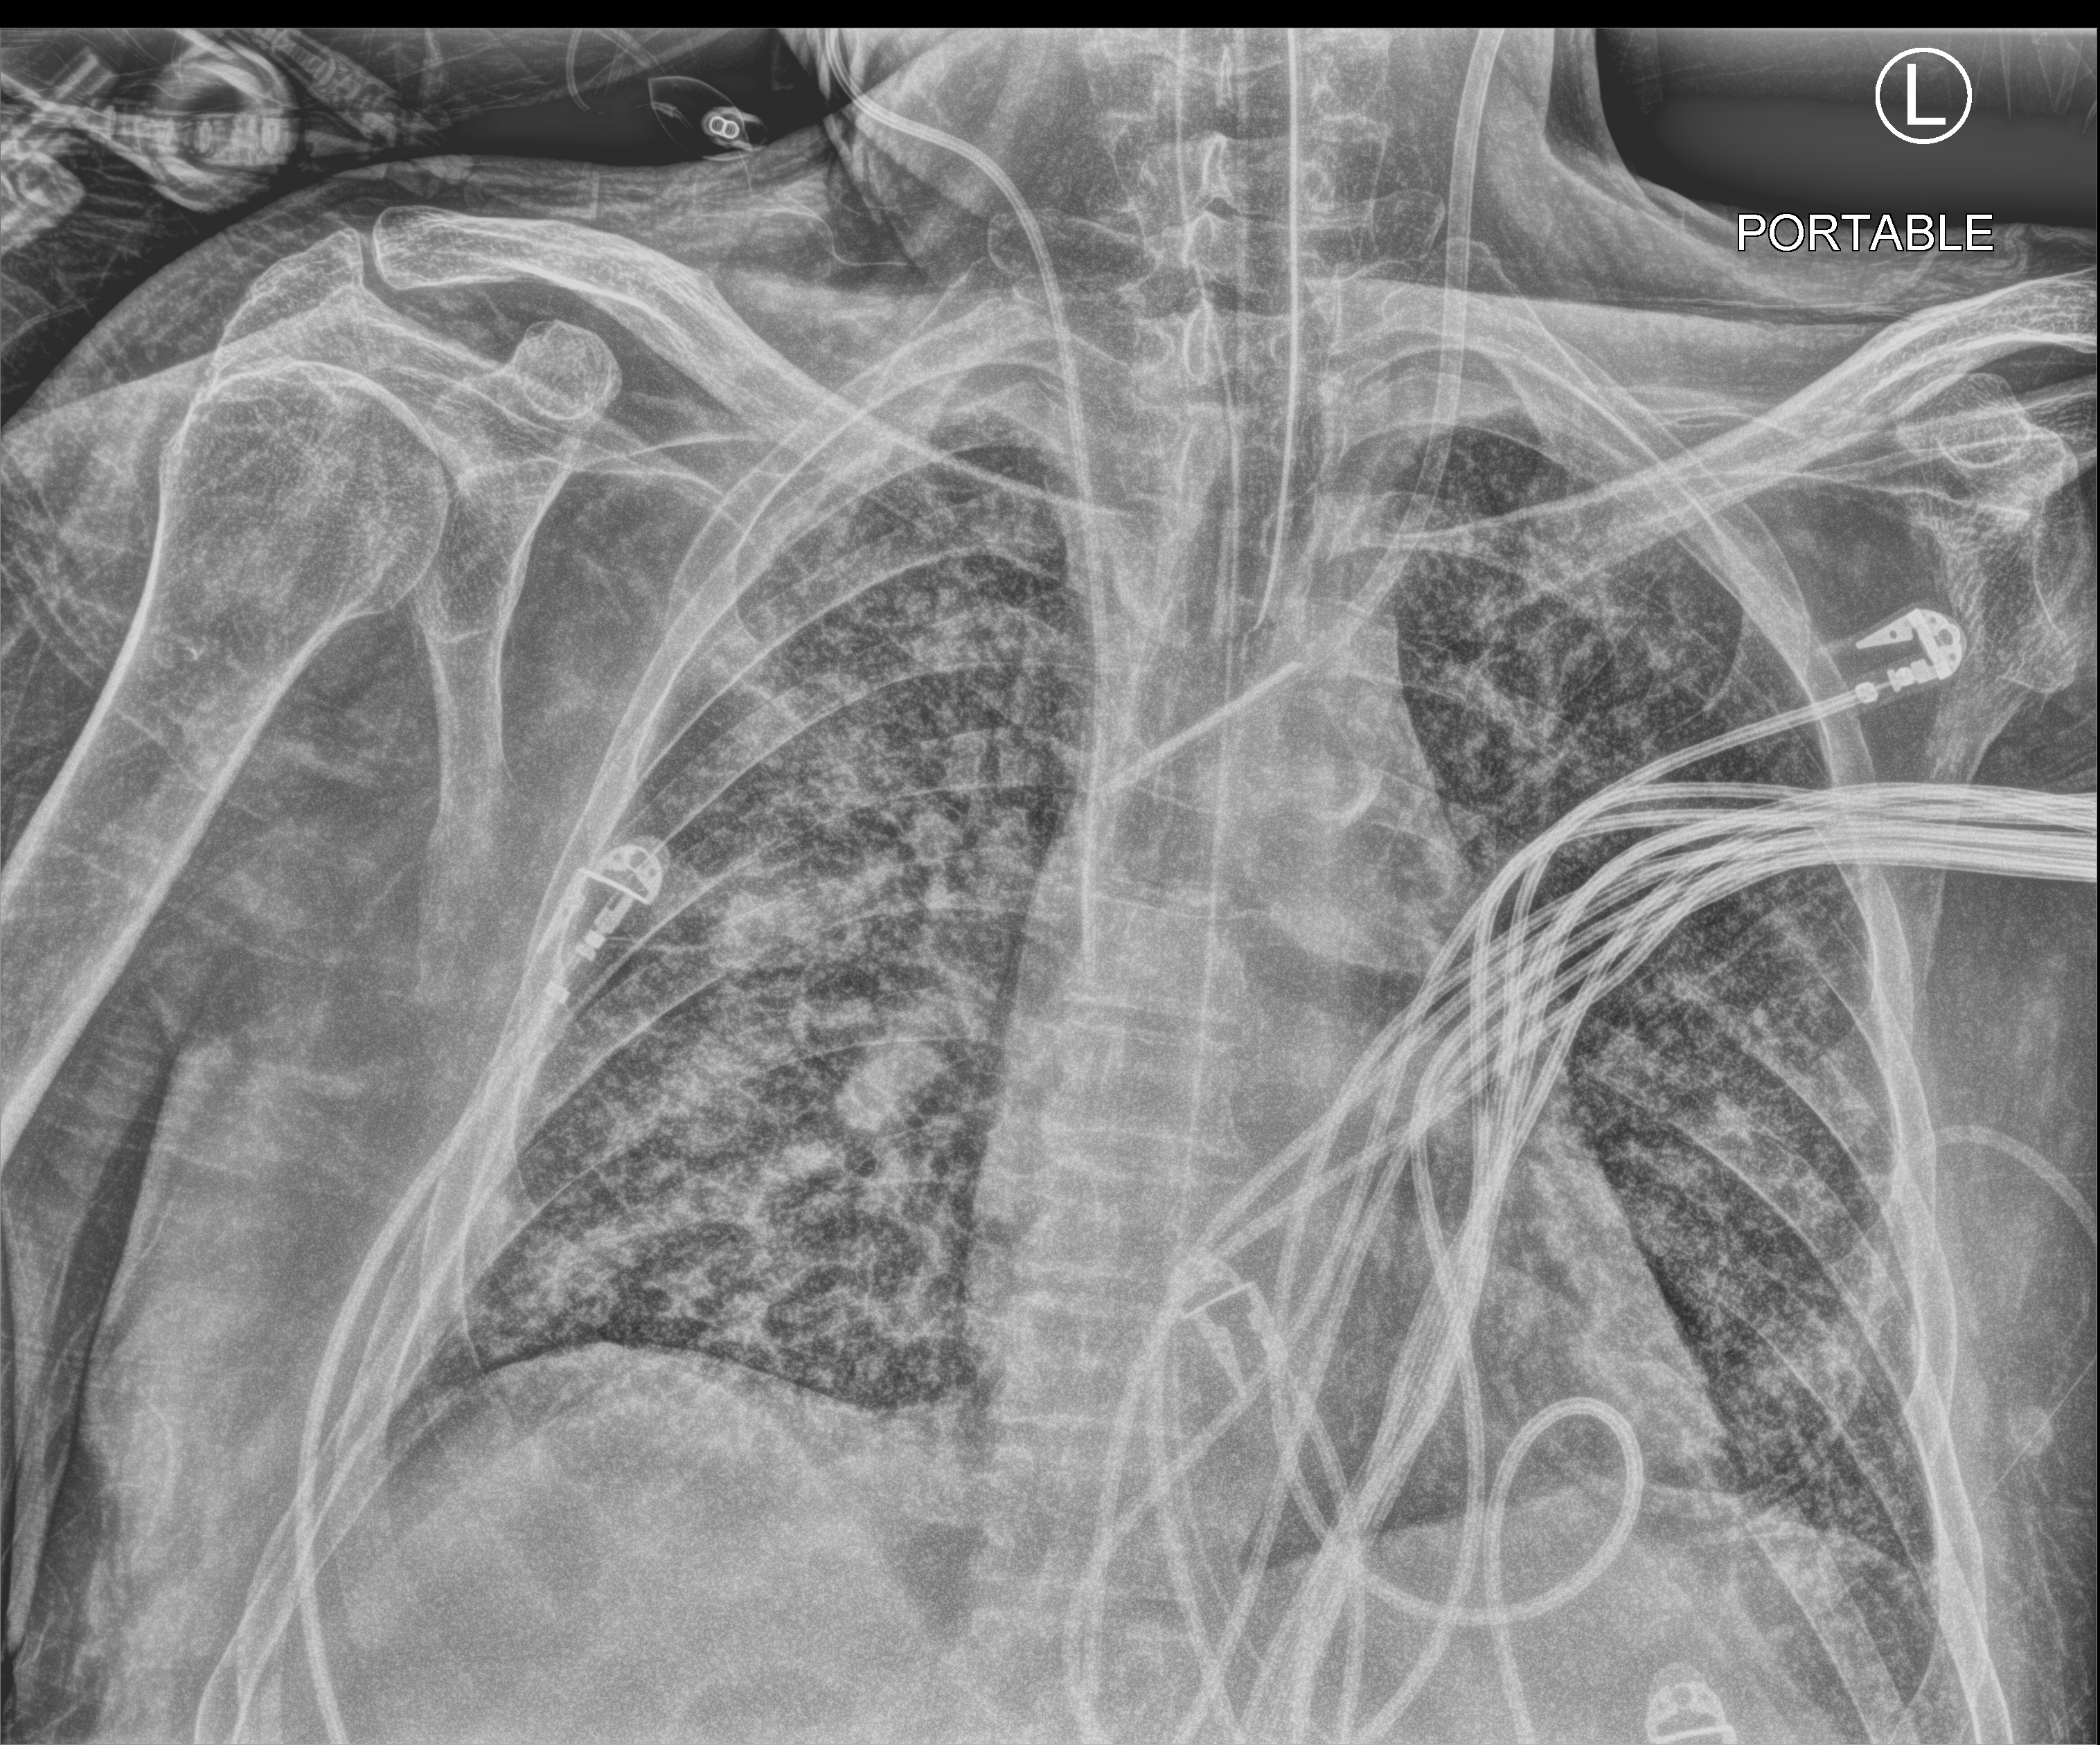
Portable chest radiograph, anteroposterior (AP) projection. Male patient hospitalised with COVID-19, age 60–74 years.
Hospital-stay facts (about this admission, not read from this image; timing relative to this image not recorded): mechanically ventilated during this hospital stay: yes; admitted to intensive care during this hospital stay: yes; COPD (admission record): no.